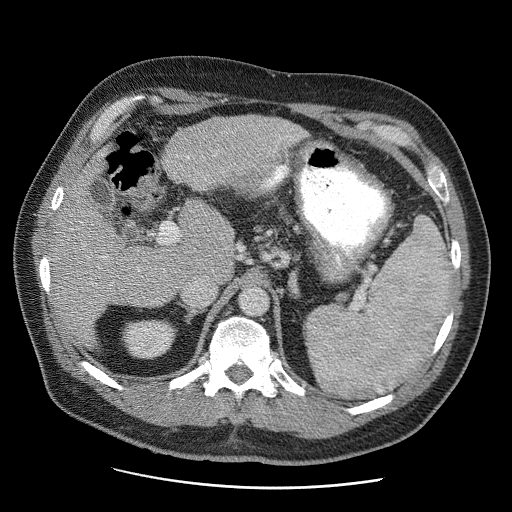
Contrast-enhanced abdominal CT (liver protocol), one axial slice. Position 29 of 81 along the scan axis. 120 kVp. Soft-tissue window (W 400 / L 40 HU). 2.5 mm slice thickness. 512 × 512 image matrix, field of view 380 × 380 mm. Case-level facts recorded for this patient, not image findings: diagnosis: hepatocellular carcinoma (patient treated with transarterial chemoembolisation; whether this scan precedes or follows treatment is not stated here); TNM stage (as recorded): Stage-IIIA; Child-Pugh class: A; tumour differentiation: moderately differentiated.
Annotated regions visible in this slice (semi-automatic segmentation, software-assisted and operator-edited):
- abdominal aorta: box from (x=239, y=287) to (x=268, y=316) px
- liver parenchyma outside the tumour (the mass and vessels are separate outlines, so this box may not span the whole liver): (x=50, y=114)–(x=306, y=348)